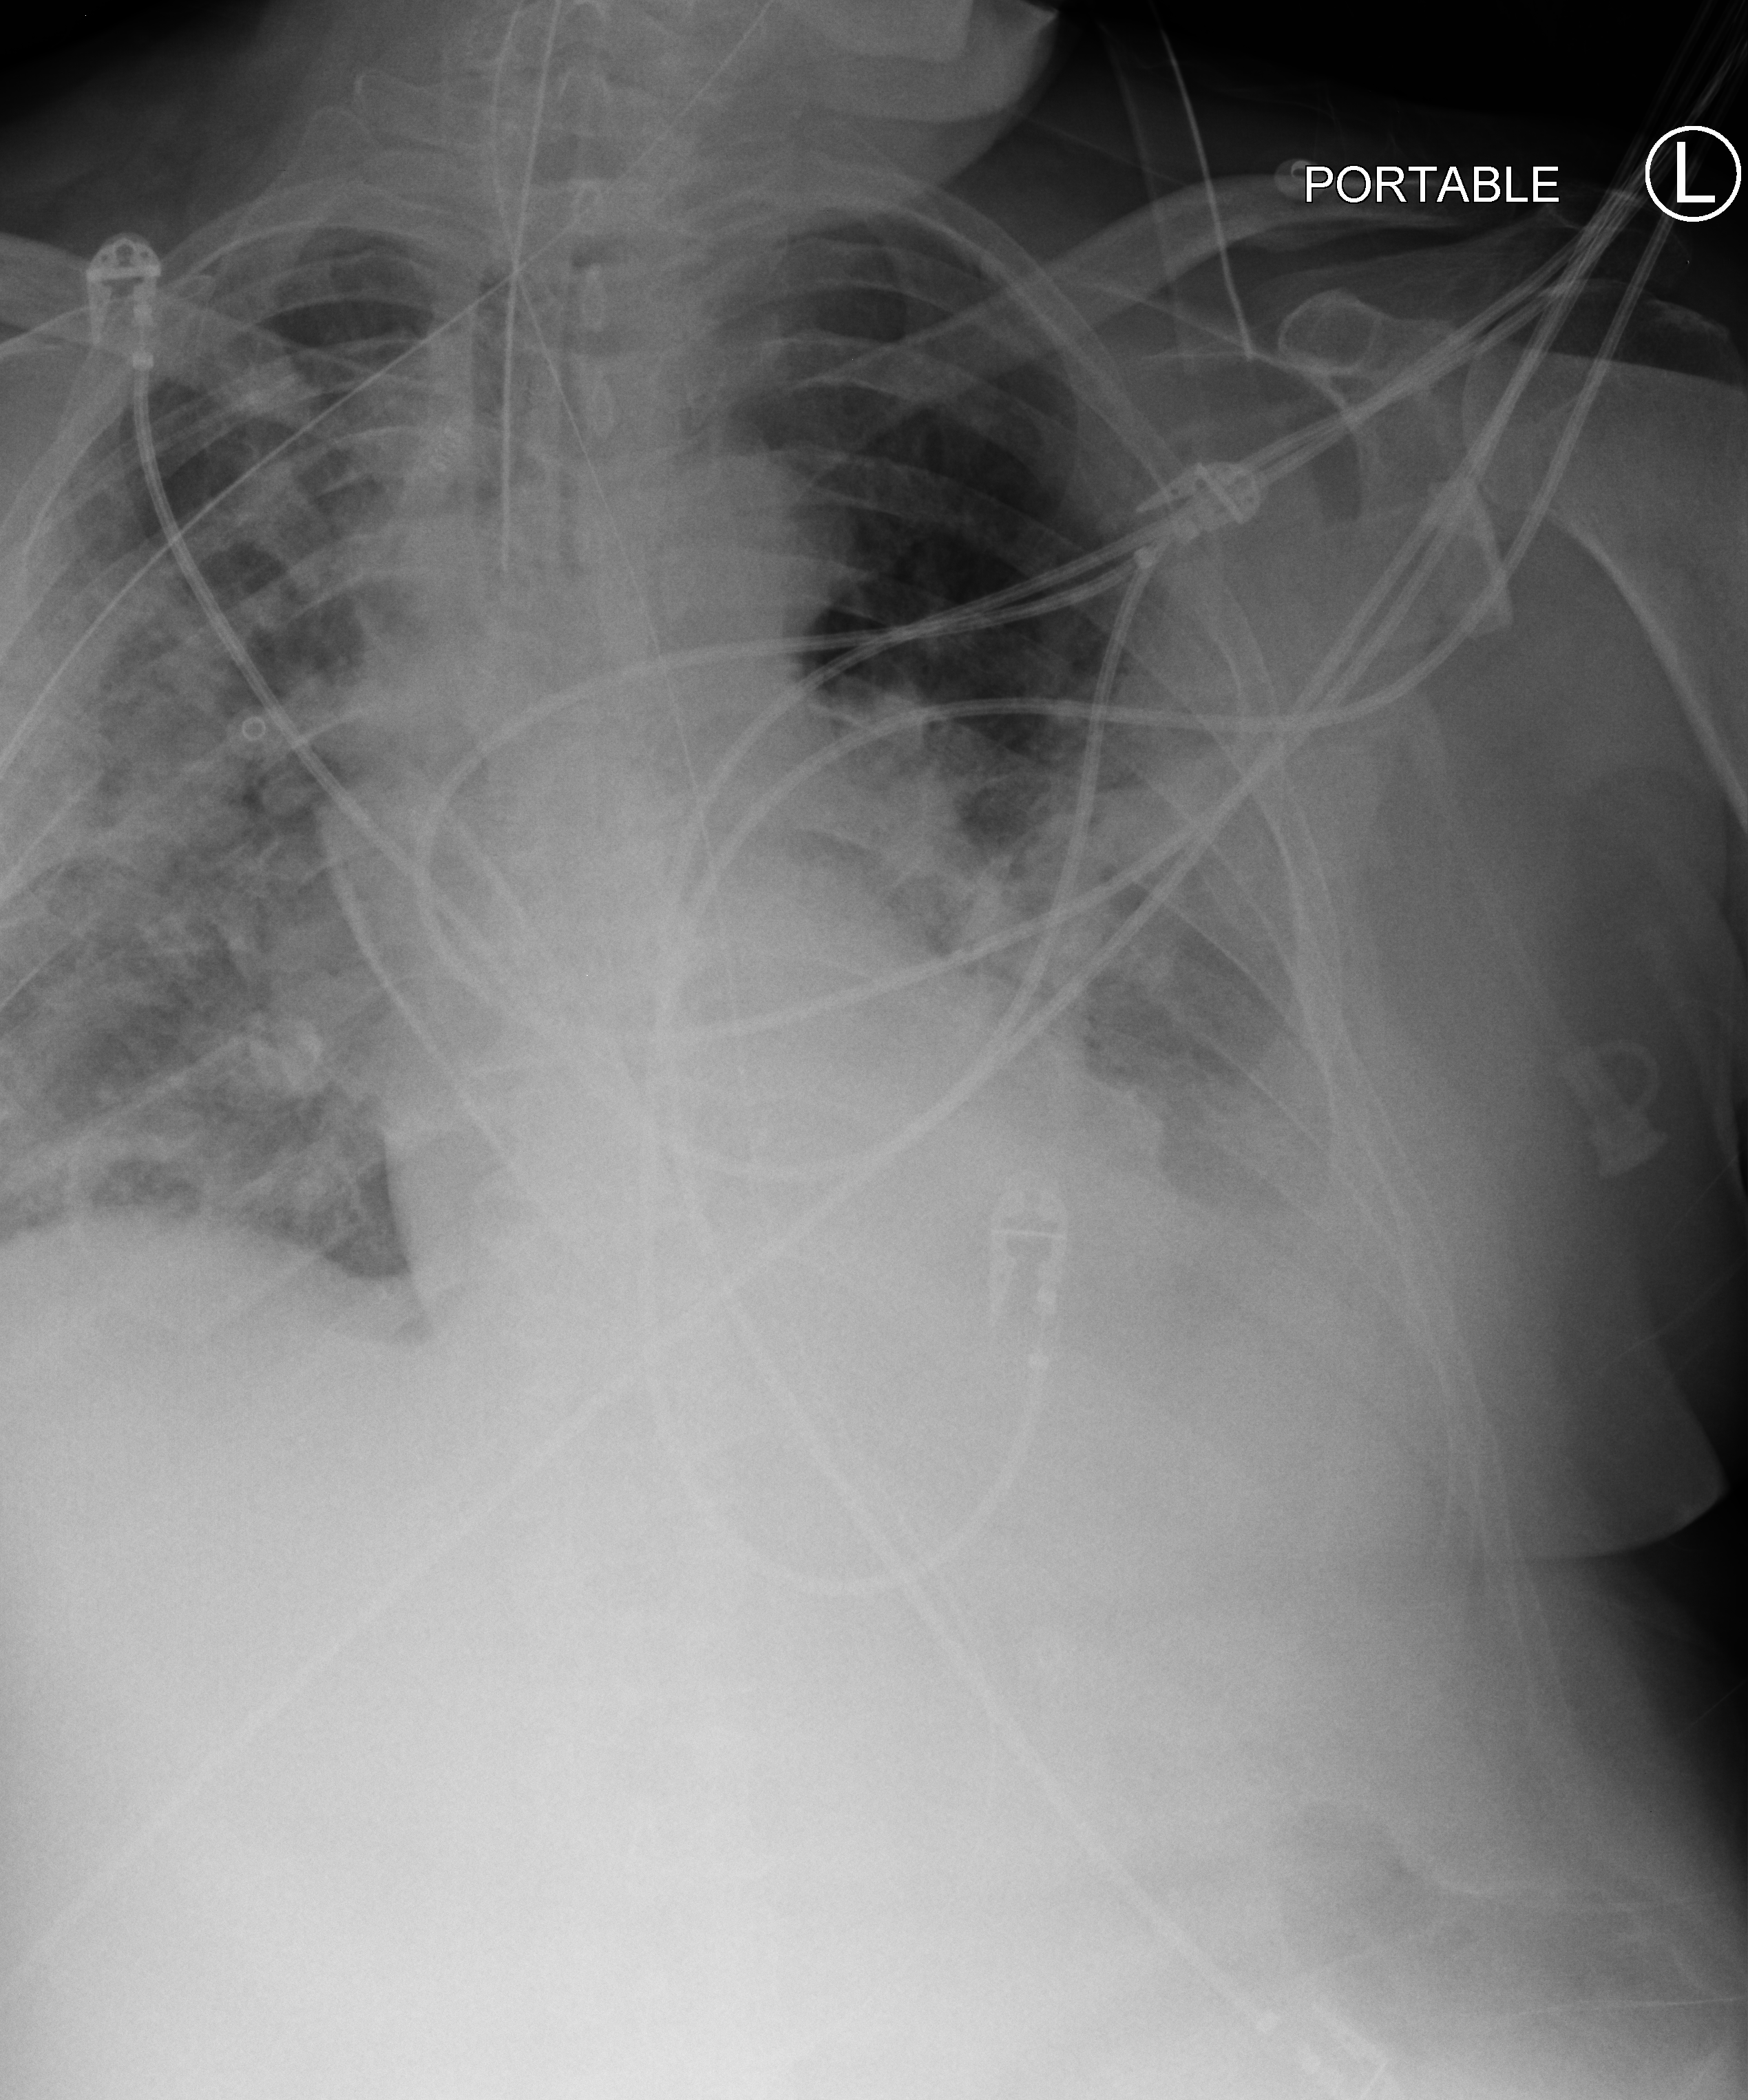
Chest X-ray (portable), anteroposterior (AP) projection. Patient hospitalised with COVID-19; male, aged 60–74 years.
Hospital-stay facts (about this admission, not read from this image; timing relative to this image not recorded):
- mechanically ventilated during this hospital stay: yes